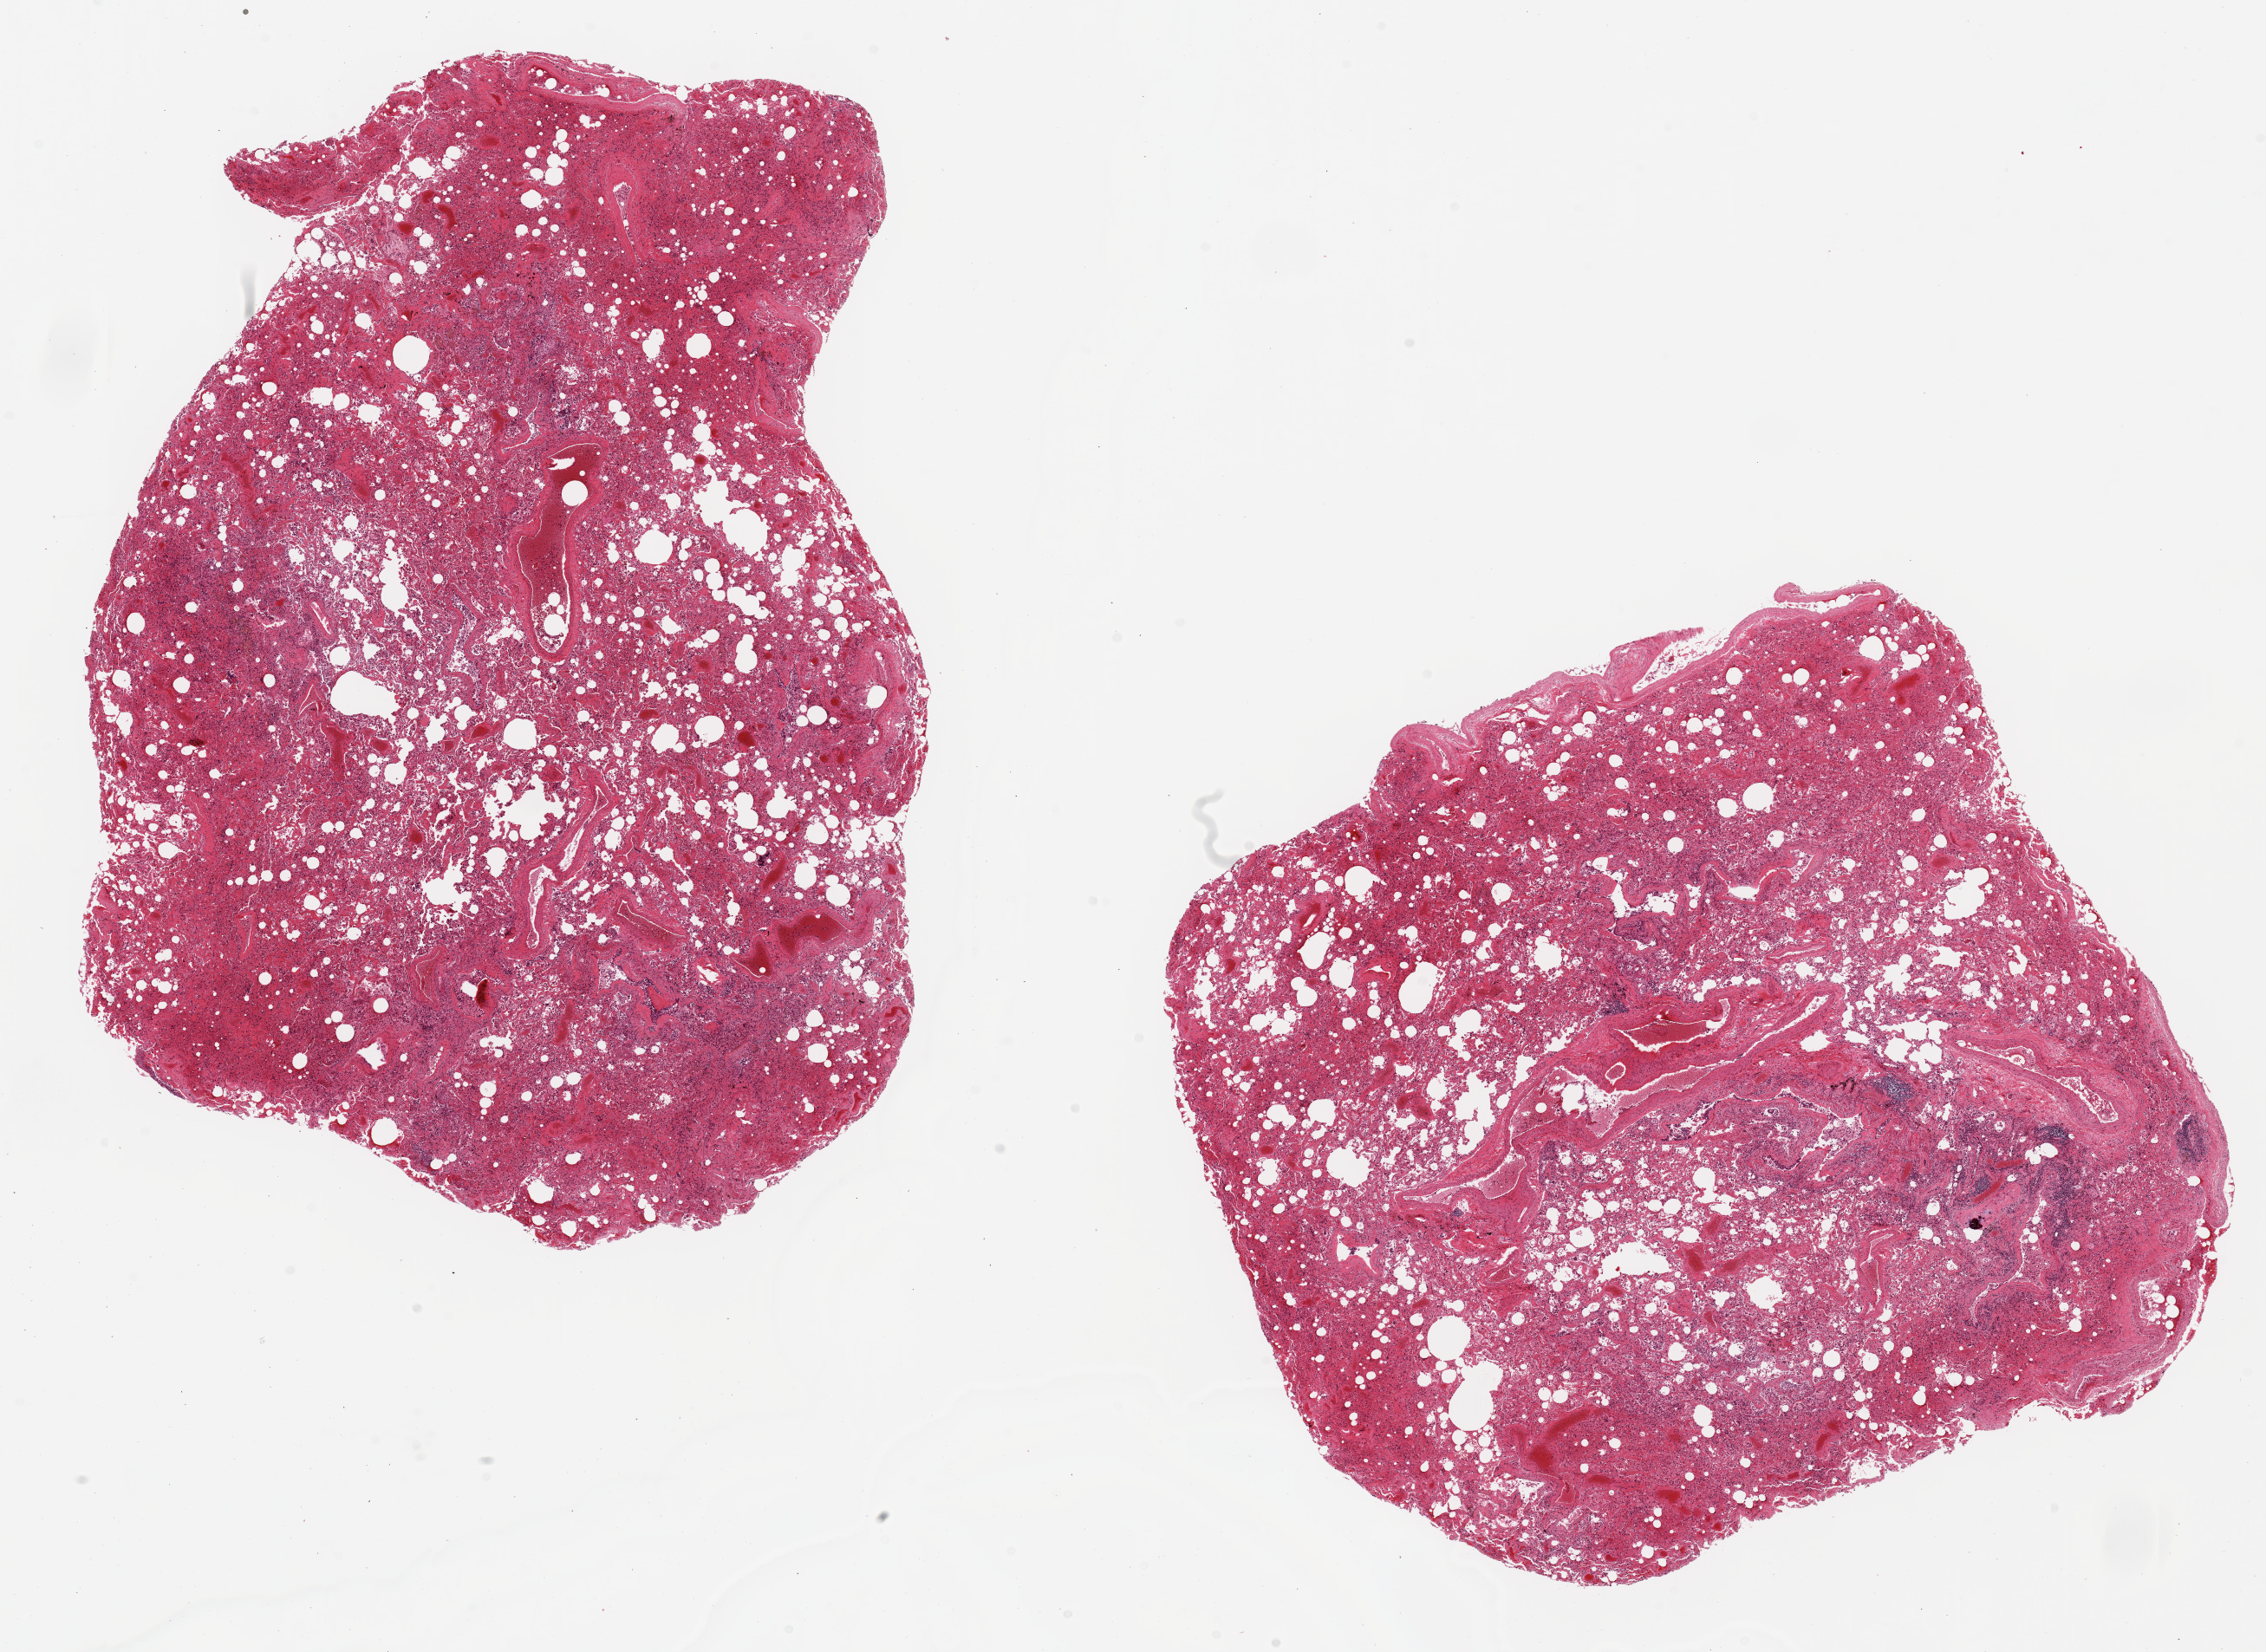
Digitized hematoxylin and eosin (H&E)-stained section — shown as a low-resolution overview of the whole scanned area (about 20.7 x 15.1 mm), PAXgene-fixed paraffin-embedded (PFPE) section, sampled site (target tissue): lung, donor tissue sample. Female donor.
* review note (as recorded): 2 aliquots, ~8x8mm. Severe congestion/hemorrhage, diffuse